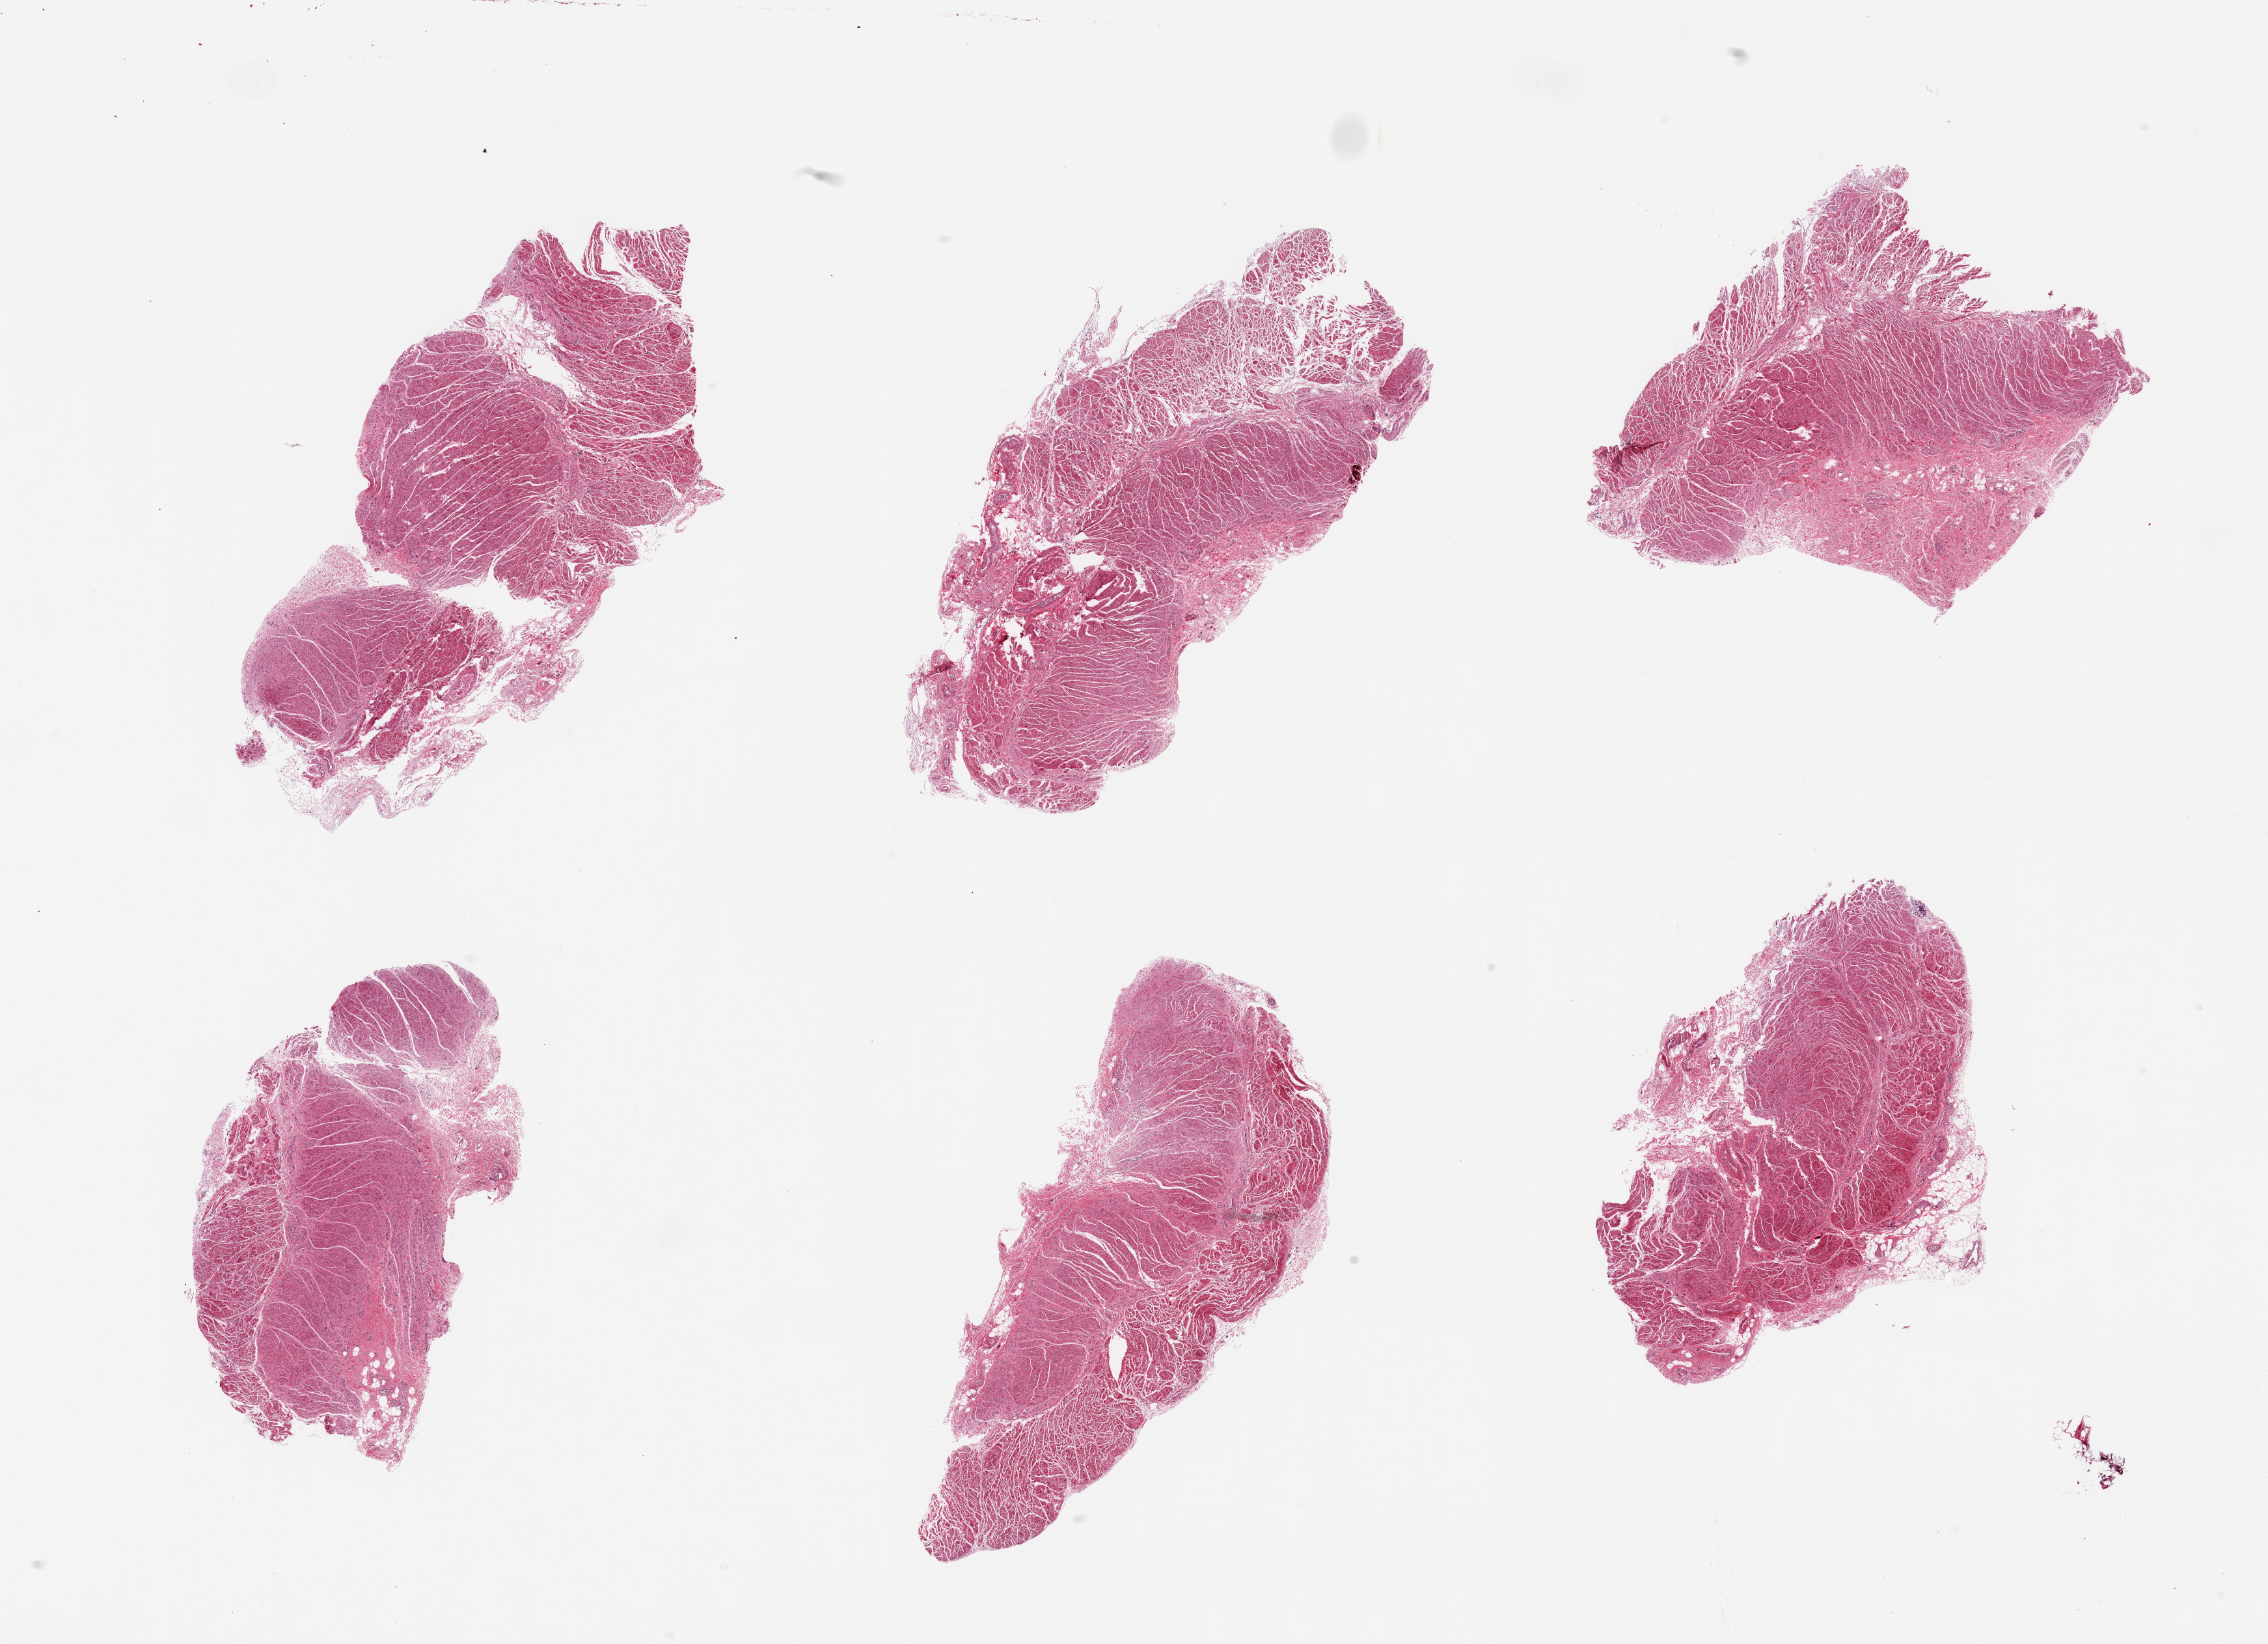
Whole-slide image, H&E stain — whole scanned area (about 27.6 x 20.0 mm, from a 20x scan) shown as a low-resolution overview, PAXgene-fixed, paraffin-embedded tissue, sampled site (target tissue): gastroesophageal junction, donor tissue sample. Male donor.
• review note (as recorded): 6 pieces; muscularis, mild to moderate autolysis